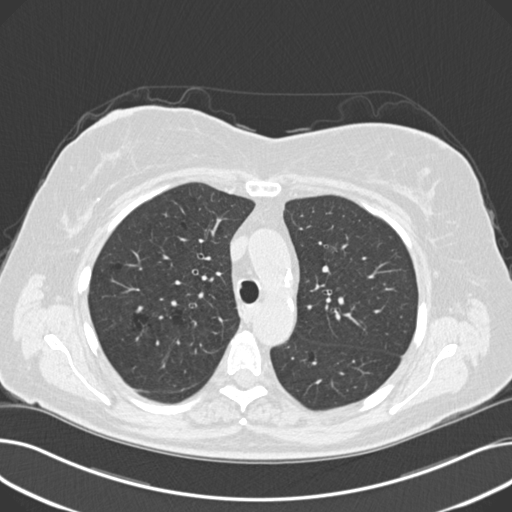
Chest CT (low-dose screening protocol), one axial image. Third screening round (two years after baseline). Lung window (W 1500 / L -600 HU). 2 mm slice thickness. Slice 67 of 203 in the series. Female participant, aged 60 years at enrolment. Current smoker at enrolment.
Expert-annotated lung lesion, bounding box <308,231,365,273> (left, top, right, bottom; pixels). The screening reader recorded 8 non-calcified nodules or masses ≥4 mm on this exam; which of them this box marks is not recorded. Participant outcome: lung cancer diagnosed 176 days after this screen — non-small cell carcinoma, left upper lobe, poorly differentiated (G3), stage IB (AJCC 6th edition), 7 mm at pathology.